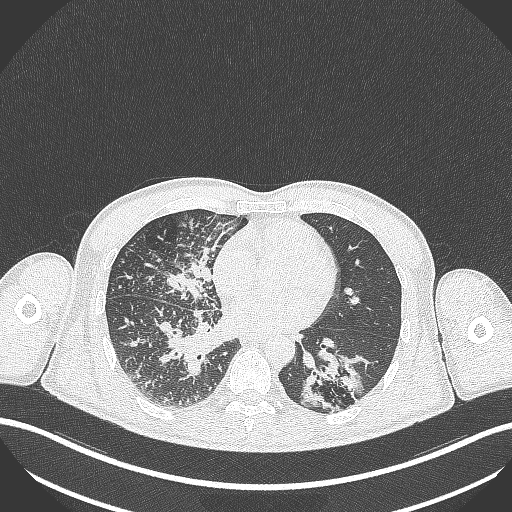
Chest CT, one axial slice; position 133 of 348 along the scan axis; 120 kVp; lung window (W 1500 / L -600 HU); 512 × 512 image matrix, field of view 400 × 400 mm. Male patient, age 49 years. From the clinical record (not read from this slice): clinical TNM (as recorded): T2b N1 M0.
Structures marked on this image (rectangle marked by the reading radiologist):
- lung tumour (recorded histology: adenocarcinoma): bounding box <295,343,371,407> (left, top, right, bottom; pixels)